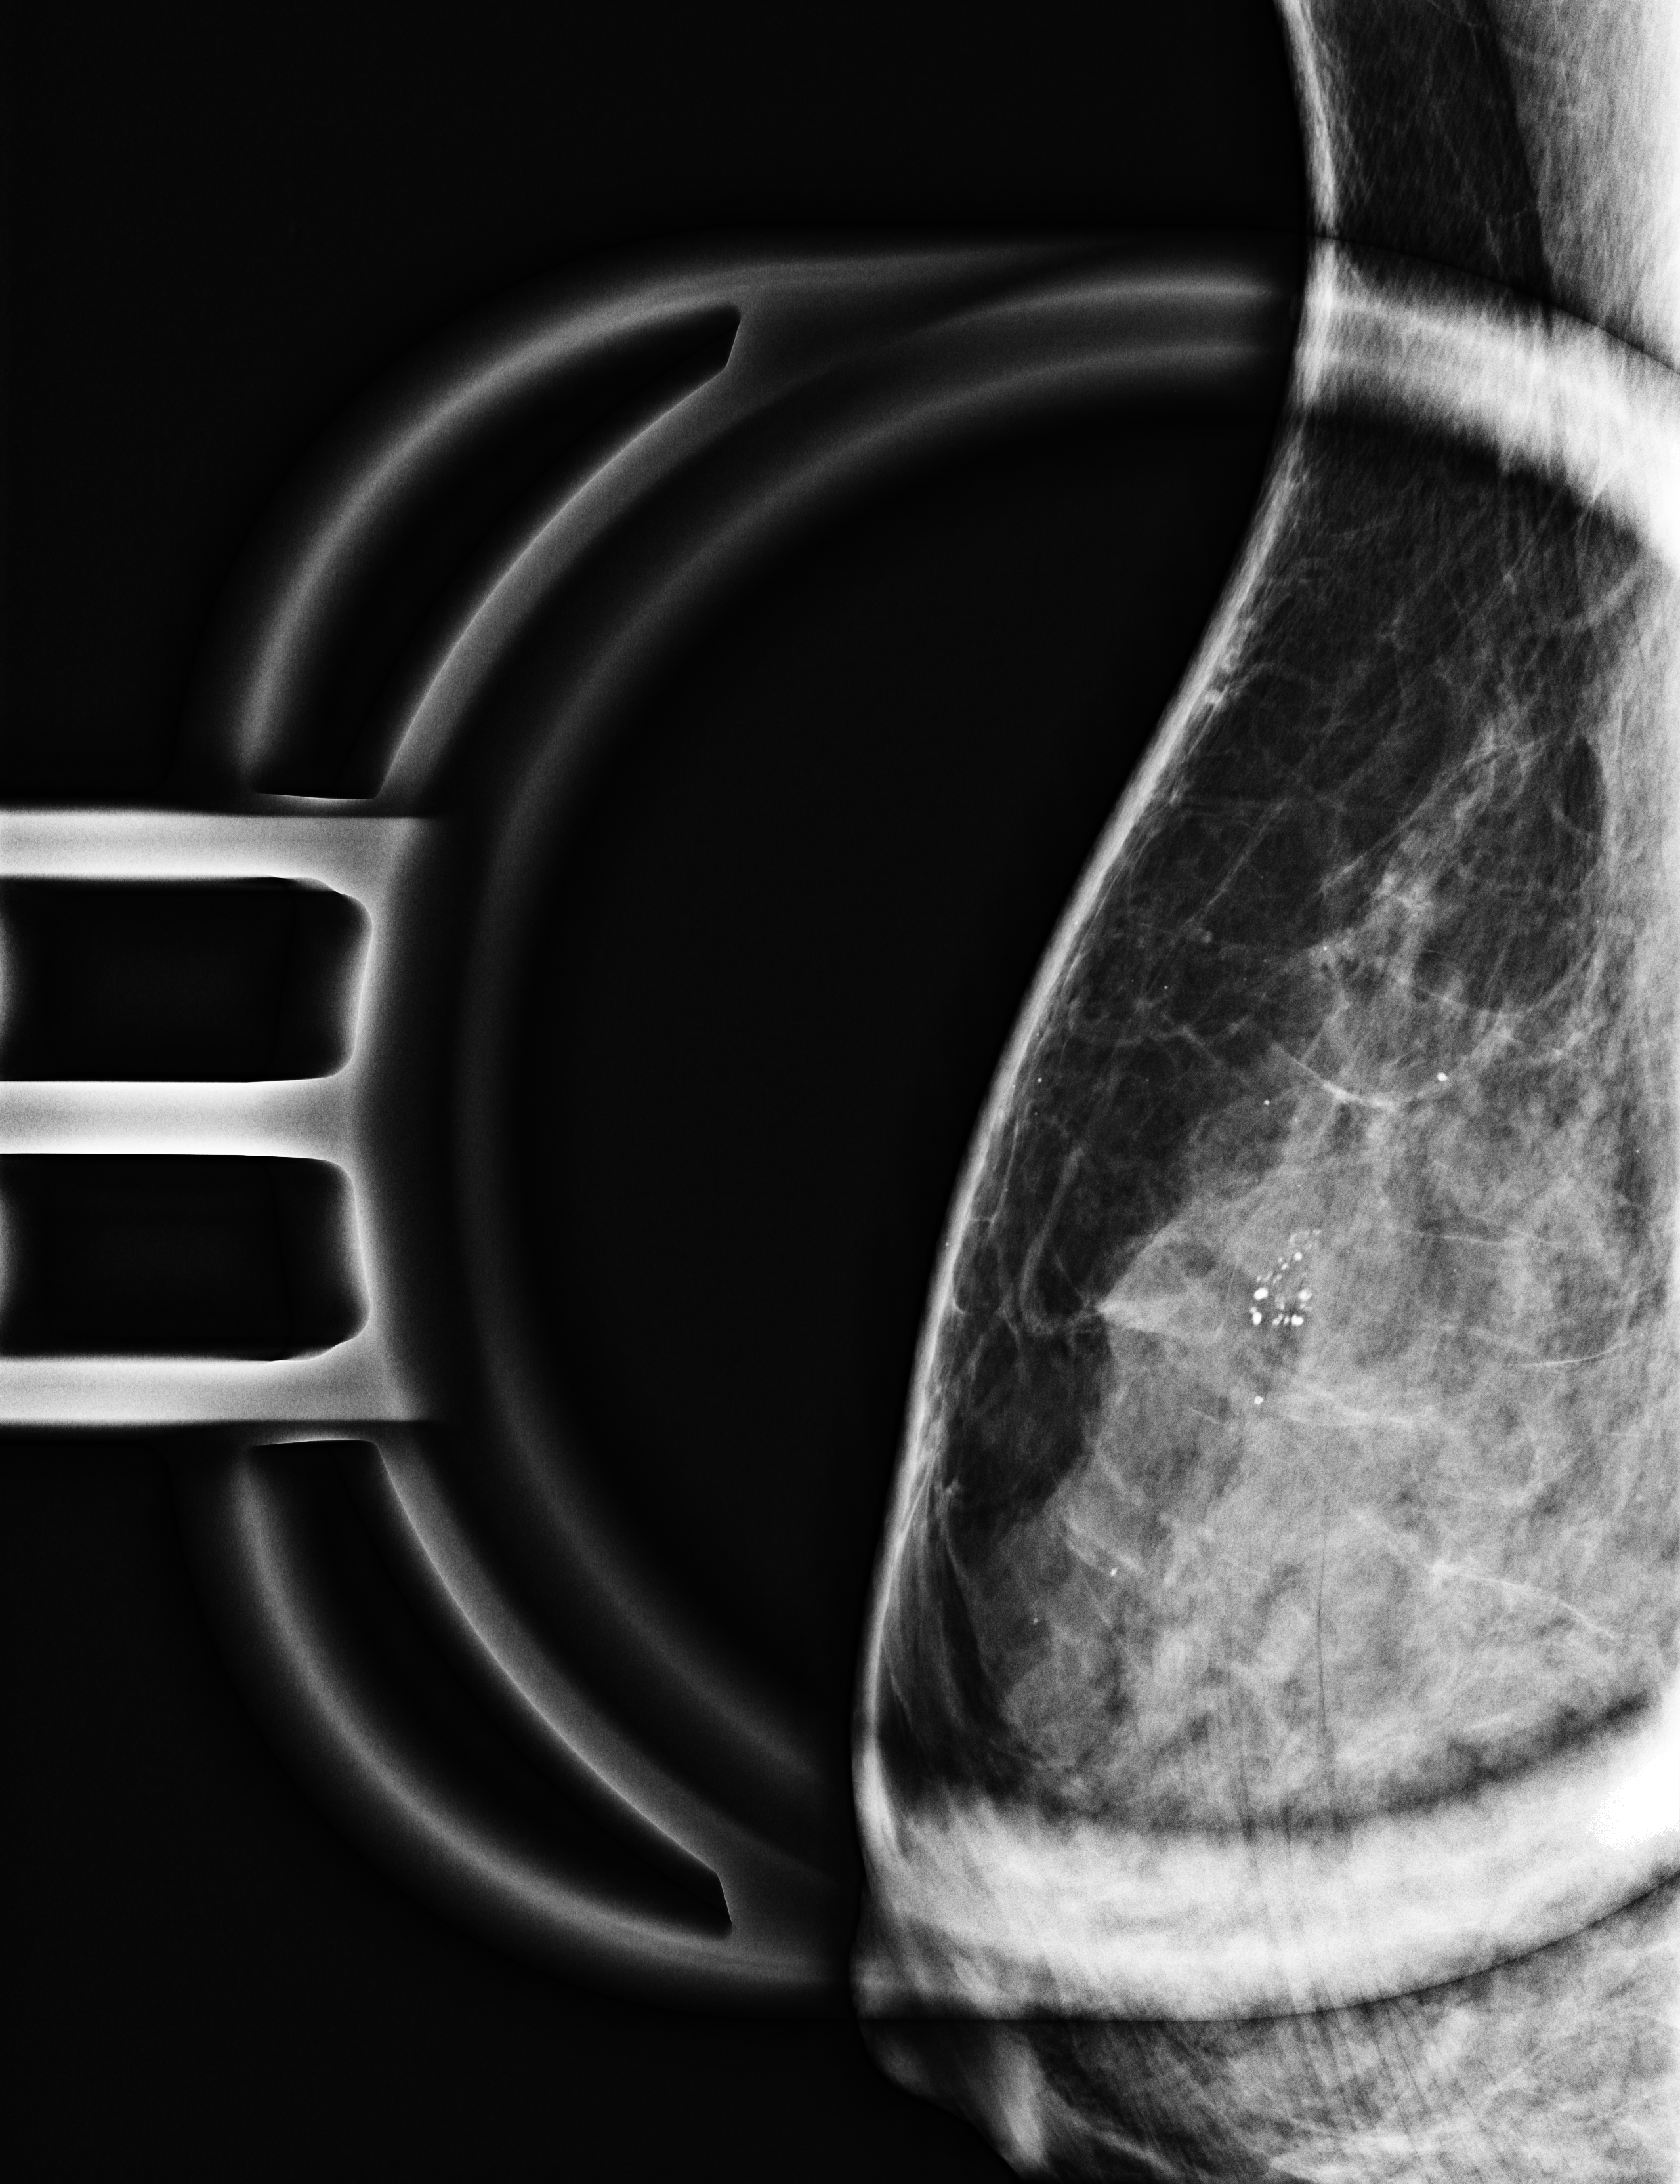
Additional work-up view, compressed breast thickness 42 mm, system: Selenia Dimensions. Patient aged 58 years (female).
Image type: full-field digital mammogram. Breast: right. Projection: mediolateral (ML) view, magnification.